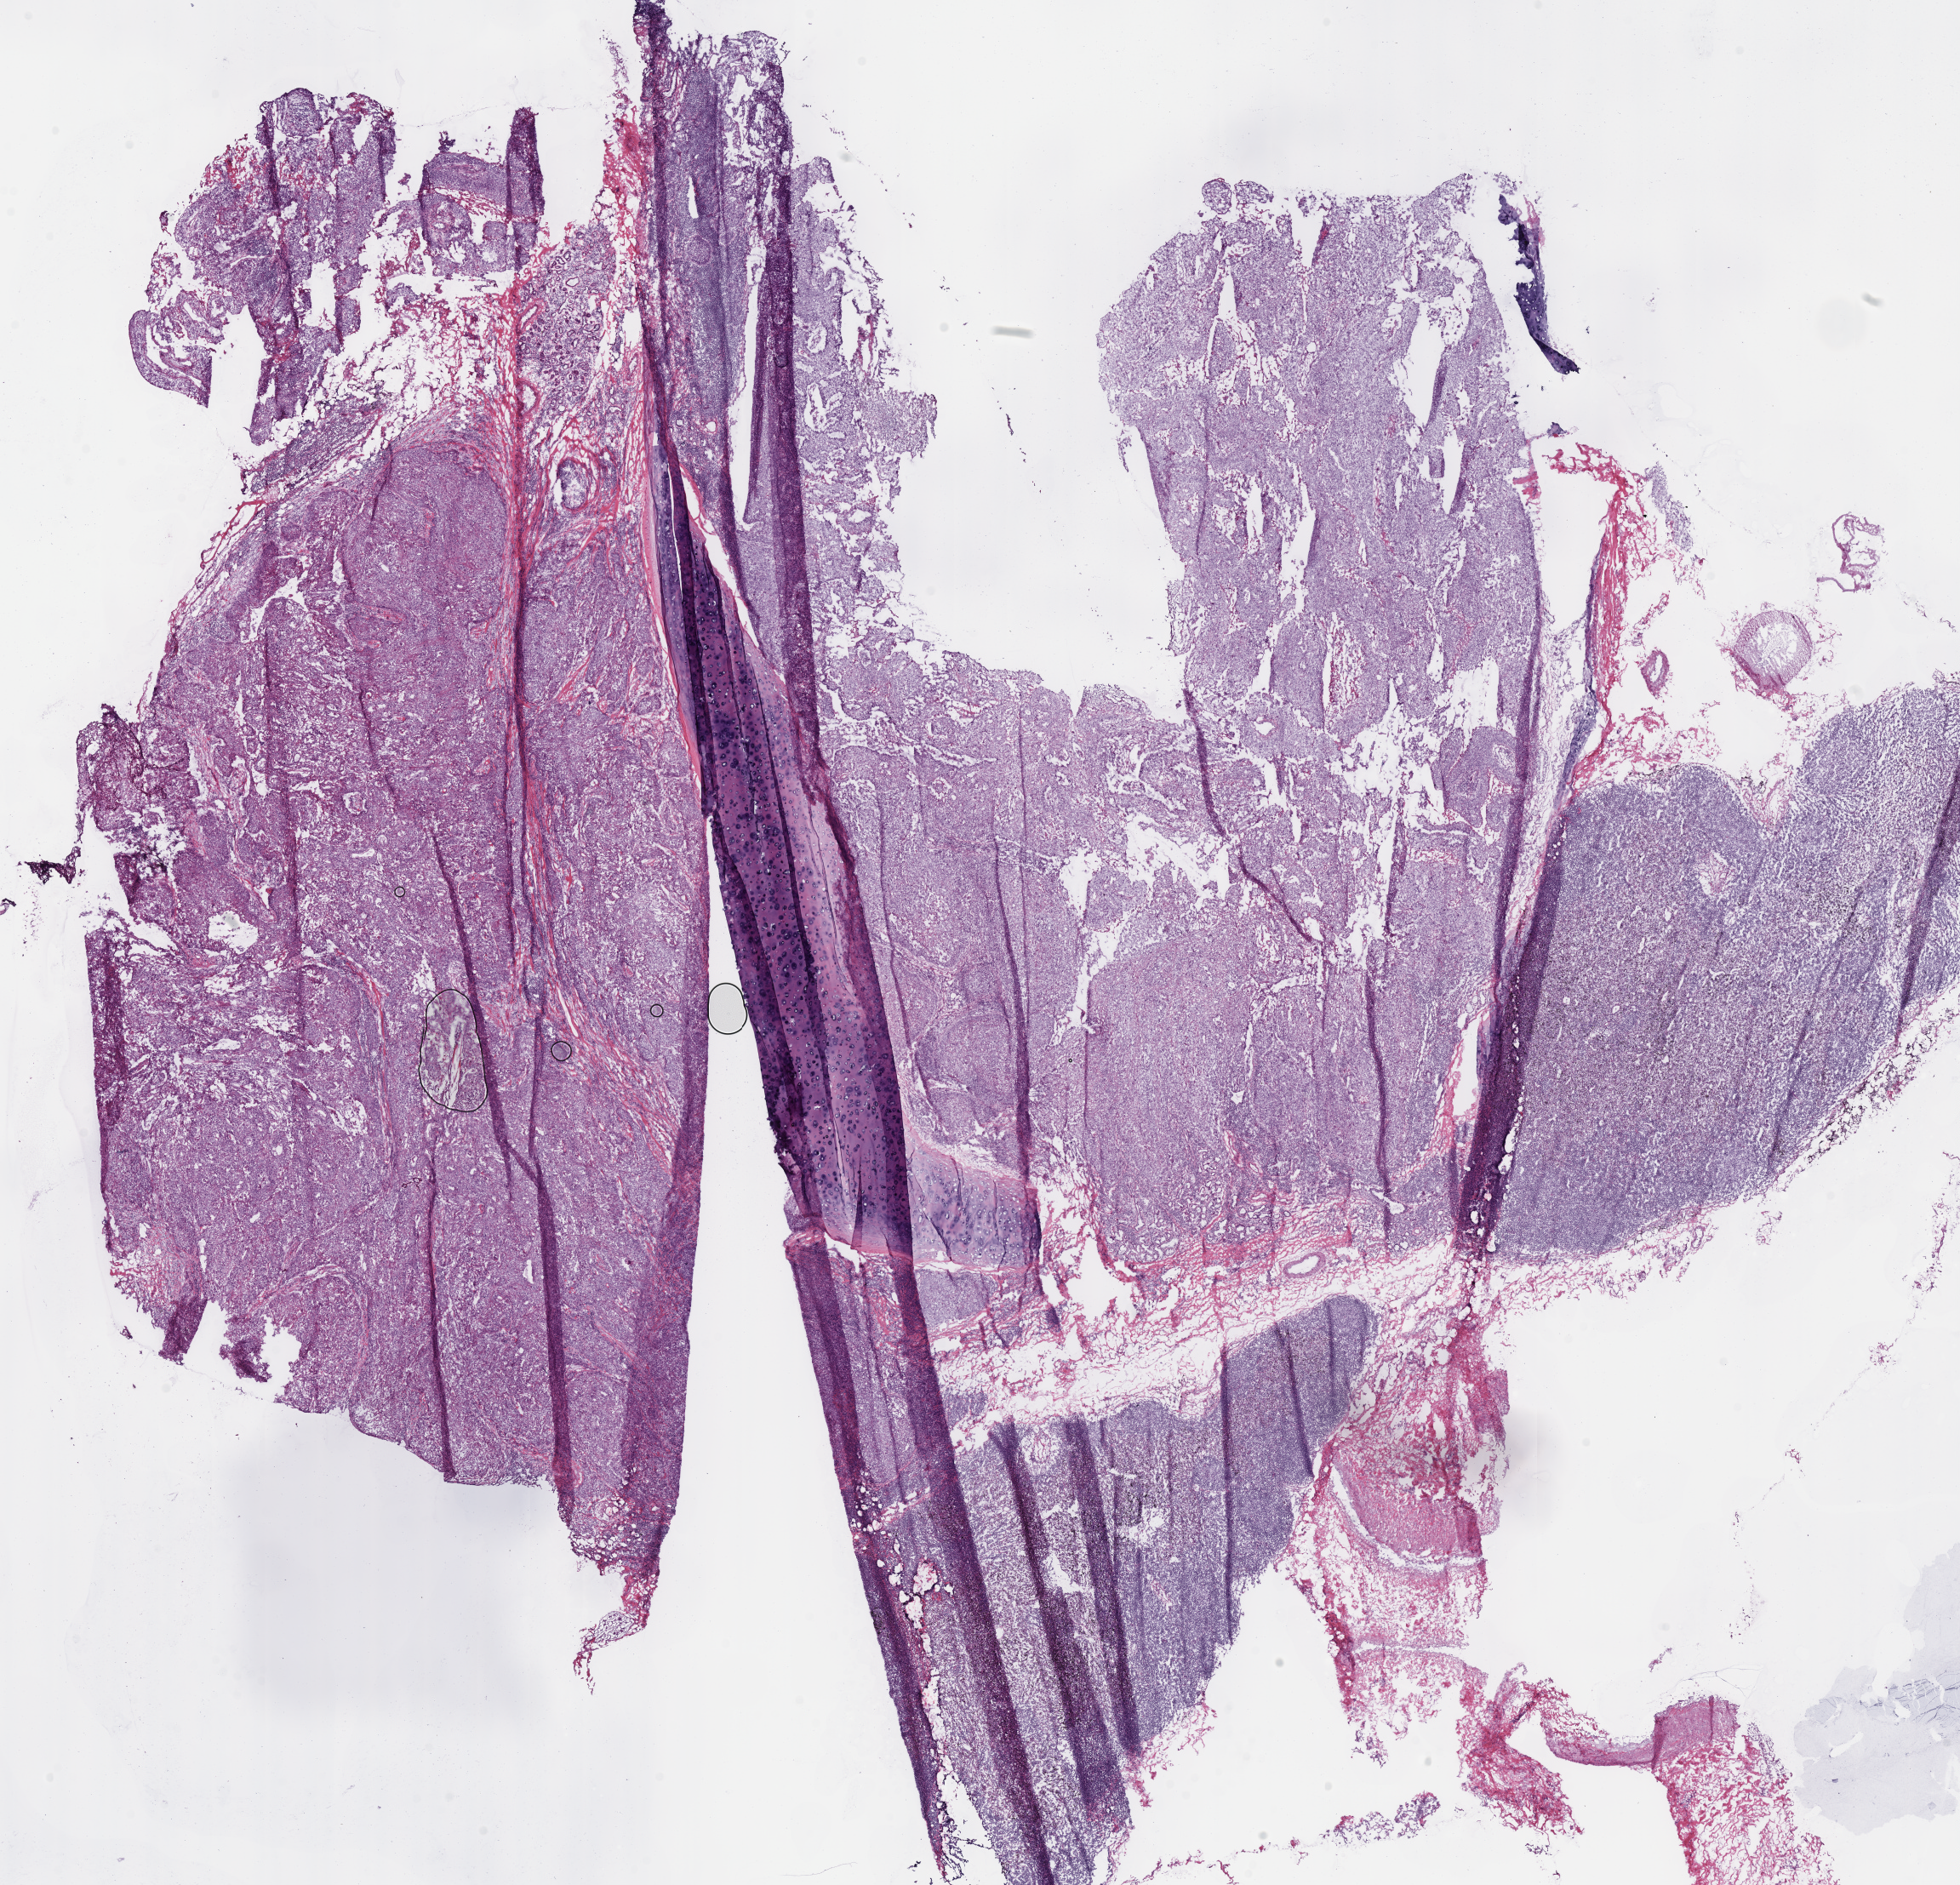
Digitized Hematoxylin and eosin (H&E) stained tissue section (whole slide) — low-resolution overview of the scanned area, about 18.1 x 17.4 mm; frozen section from the bottom of the tissue portion; lung, primary tumour sample. Male, age 63 years at initial diagnosis. Slide review estimates, as recorded: tumour cells 70%, tumour nuclei 70%, normal cells 0%, stromal cells 15%, necrosis 15%.
Pathologic diagnosis: Squamous cell carcinoma, NOS (upper lobe, lung). Laterality: left. AJCC pathologic stage: IA (7th edition).